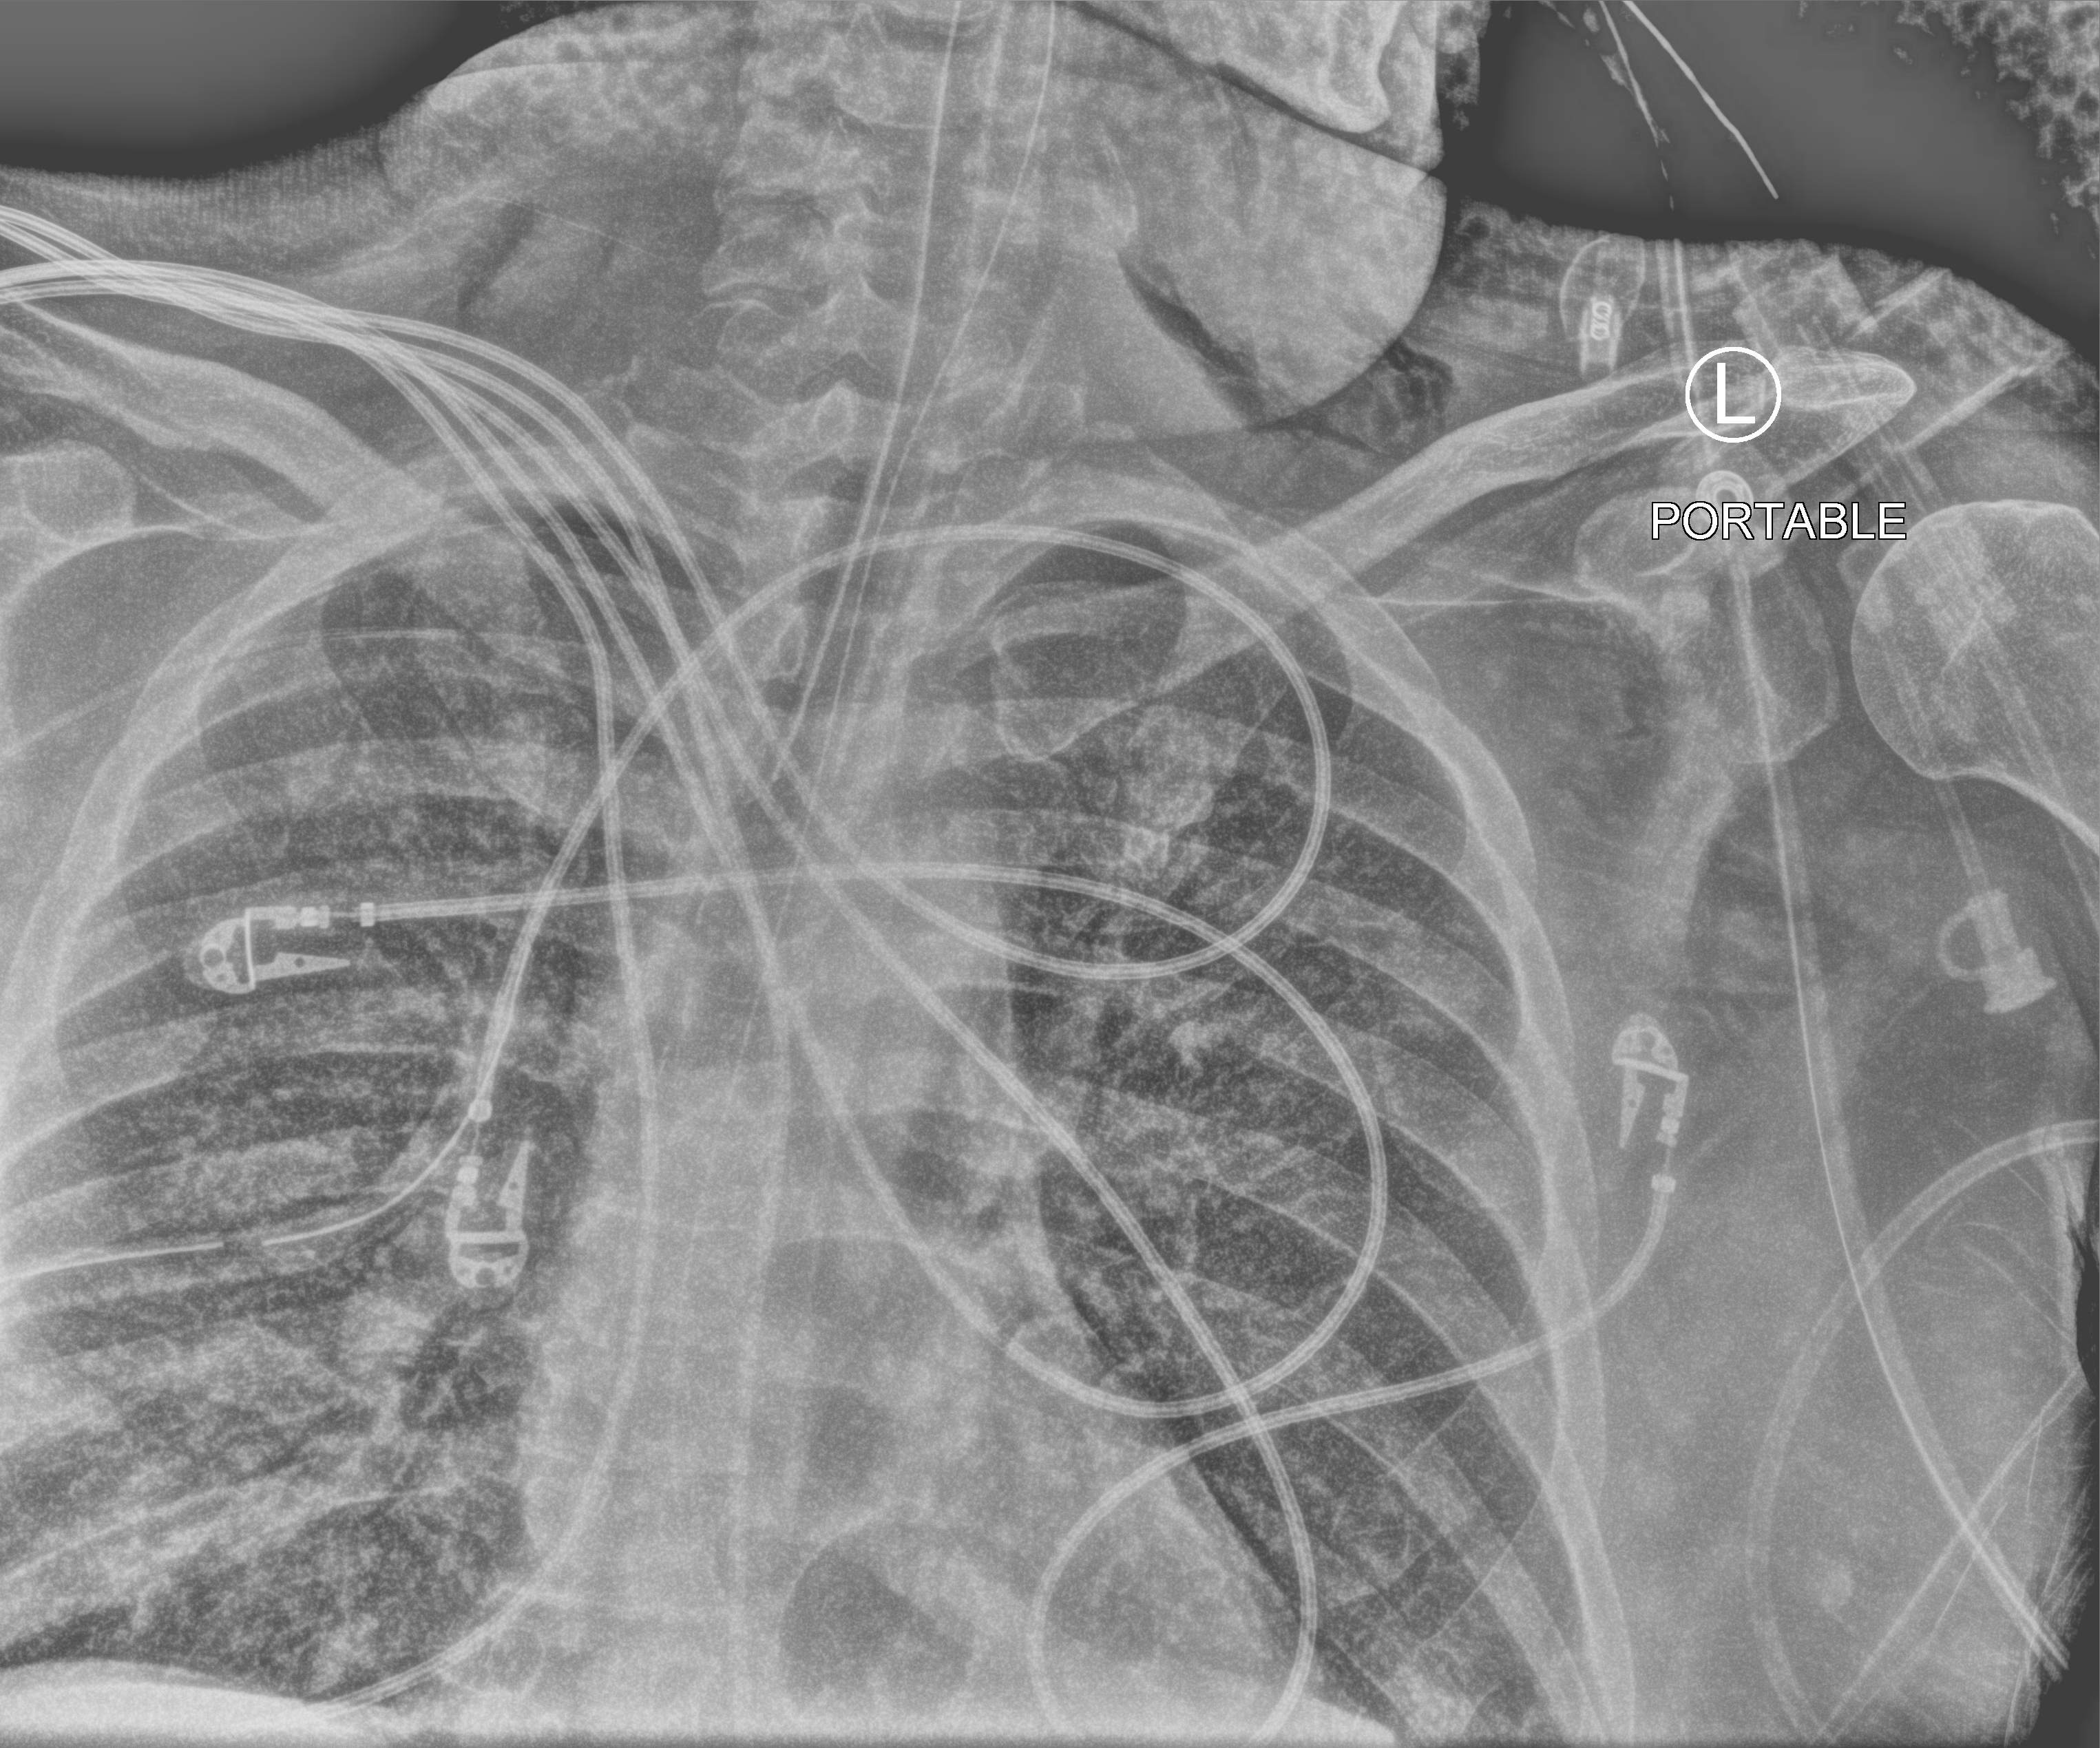
Chest X-ray (portable), anteroposterior (AP) projection. Adult patient hospitalised with COVID-19, age 18–59 years.
Hospital-stay facts (about this admission, not read from this image; timing relative to this image not recorded):
- admitted to intensive care during this hospital stay: yes